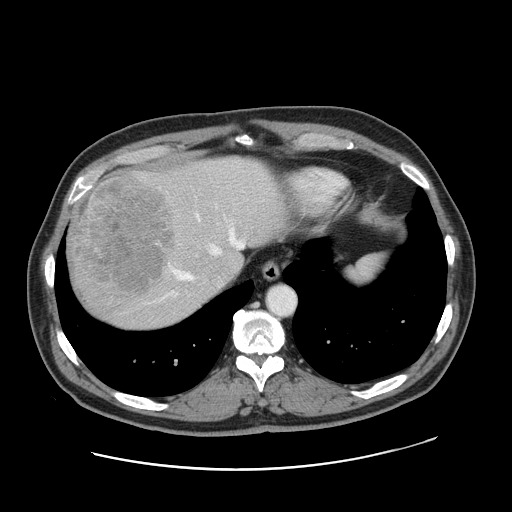
Contrast-enhanced abdominal CT, one axial slice. Slice 135 of 178 in the series (ordered by position). Intravenous contrast given. Soft-tissue window (W 400 / L 40 HU). 512 × 512 image matrix. Male patient, age 63 years. From the clinical record (not read from this slice): diagnosis: colorectal cancer liver metastases, imaged before liver resection; multiple liver metastases: yes; largest metastasis: 8 cm; disease in both lobes: yes.
Outlined on this slice (manually delineated by an expert):
- hepatic veins: bounding box [x1, y1, x2, y2] px = [174, 213, 245, 280]
- liver: [66, 157, 286, 330]
- planned liver remnant (the part of the liver to remain after resection): [167, 160, 286, 281]
- portal vein (with intrahepatic branches): [158, 242, 160, 244]
- liver metastasis: [68, 173, 176, 297]